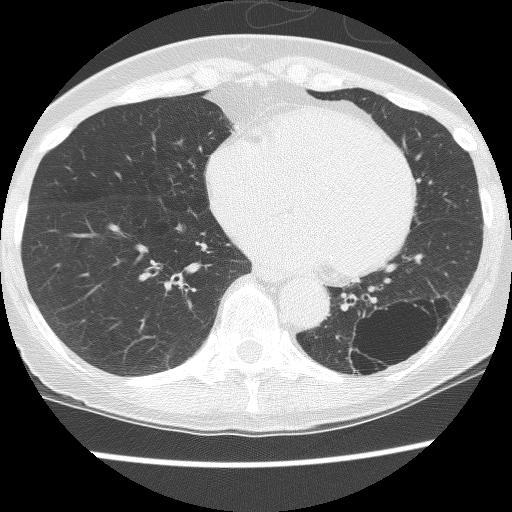
Axial slice from a low-dose chest CT screening exam; third screening round (two years after baseline); lung window (W 1500 / L -600 HU); lung (sharp) reconstruction kernel (BONE); slice 85 of 130 in the series. Female, age 61 years at enrolment. Current smoker at enrolment.
Expert reader's lesion annotation, bounding box (x1, y1, x2, y2) in pixels: (331, 290, 449, 389). The screening reader recorded 2 non-calcified nodules or masses ≥4 mm on this exam (left lower lobe, left lower lobe); which of them this box marks is not recorded. Later outcome: lung cancer diagnosed 166 days after this screen — non-small cell carcinoma, left lower lobe, poorly differentiated (G3), stage IB (AJCC 6th edition), 100 mm at pathology.